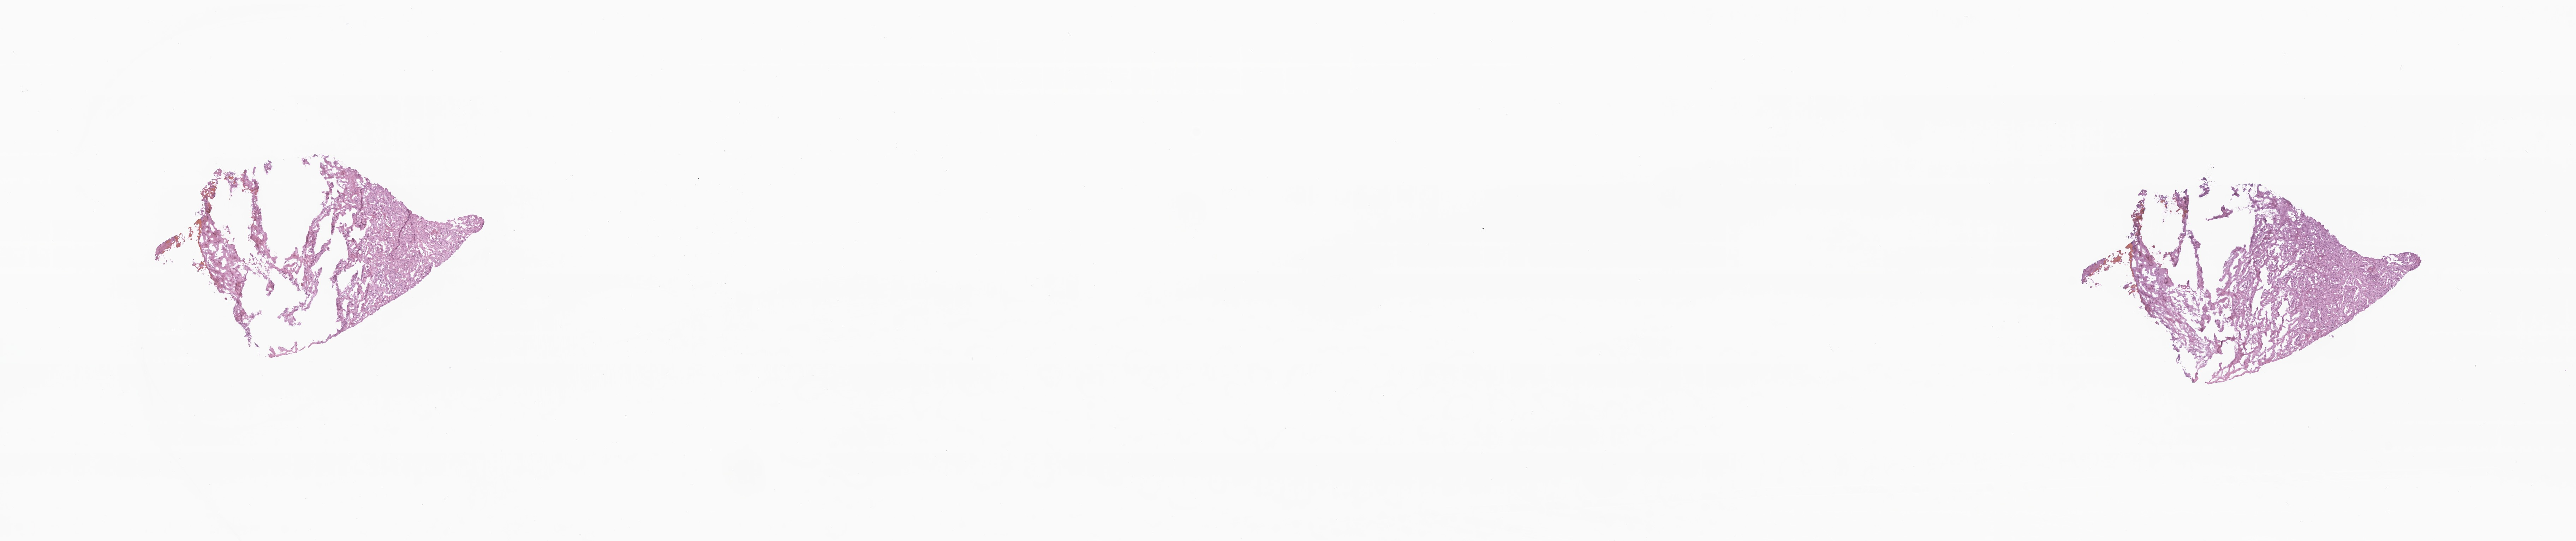
Hematoxylin and eosin (H&E) whole-slide image, low-resolution overview of the scanned area, about 30.8 x 6.5 mm. Frozen section (tissue freezing medium). Recurrent tumor. Site: brain. Patient: male, age at initial diagnosis 49 years. Composition of this section per pathologist review: tumor cells 70%, tumor nuclei 80%, stromal cells 20%, necrosis 10%, normal cells 0%. Inflammatory infiltration, as recorded: lymphocyte infiltration 0%, monocyte infiltration 0%, neutrophil infiltration 0%.
• patient diagnosis: Glioblastoma, NOS